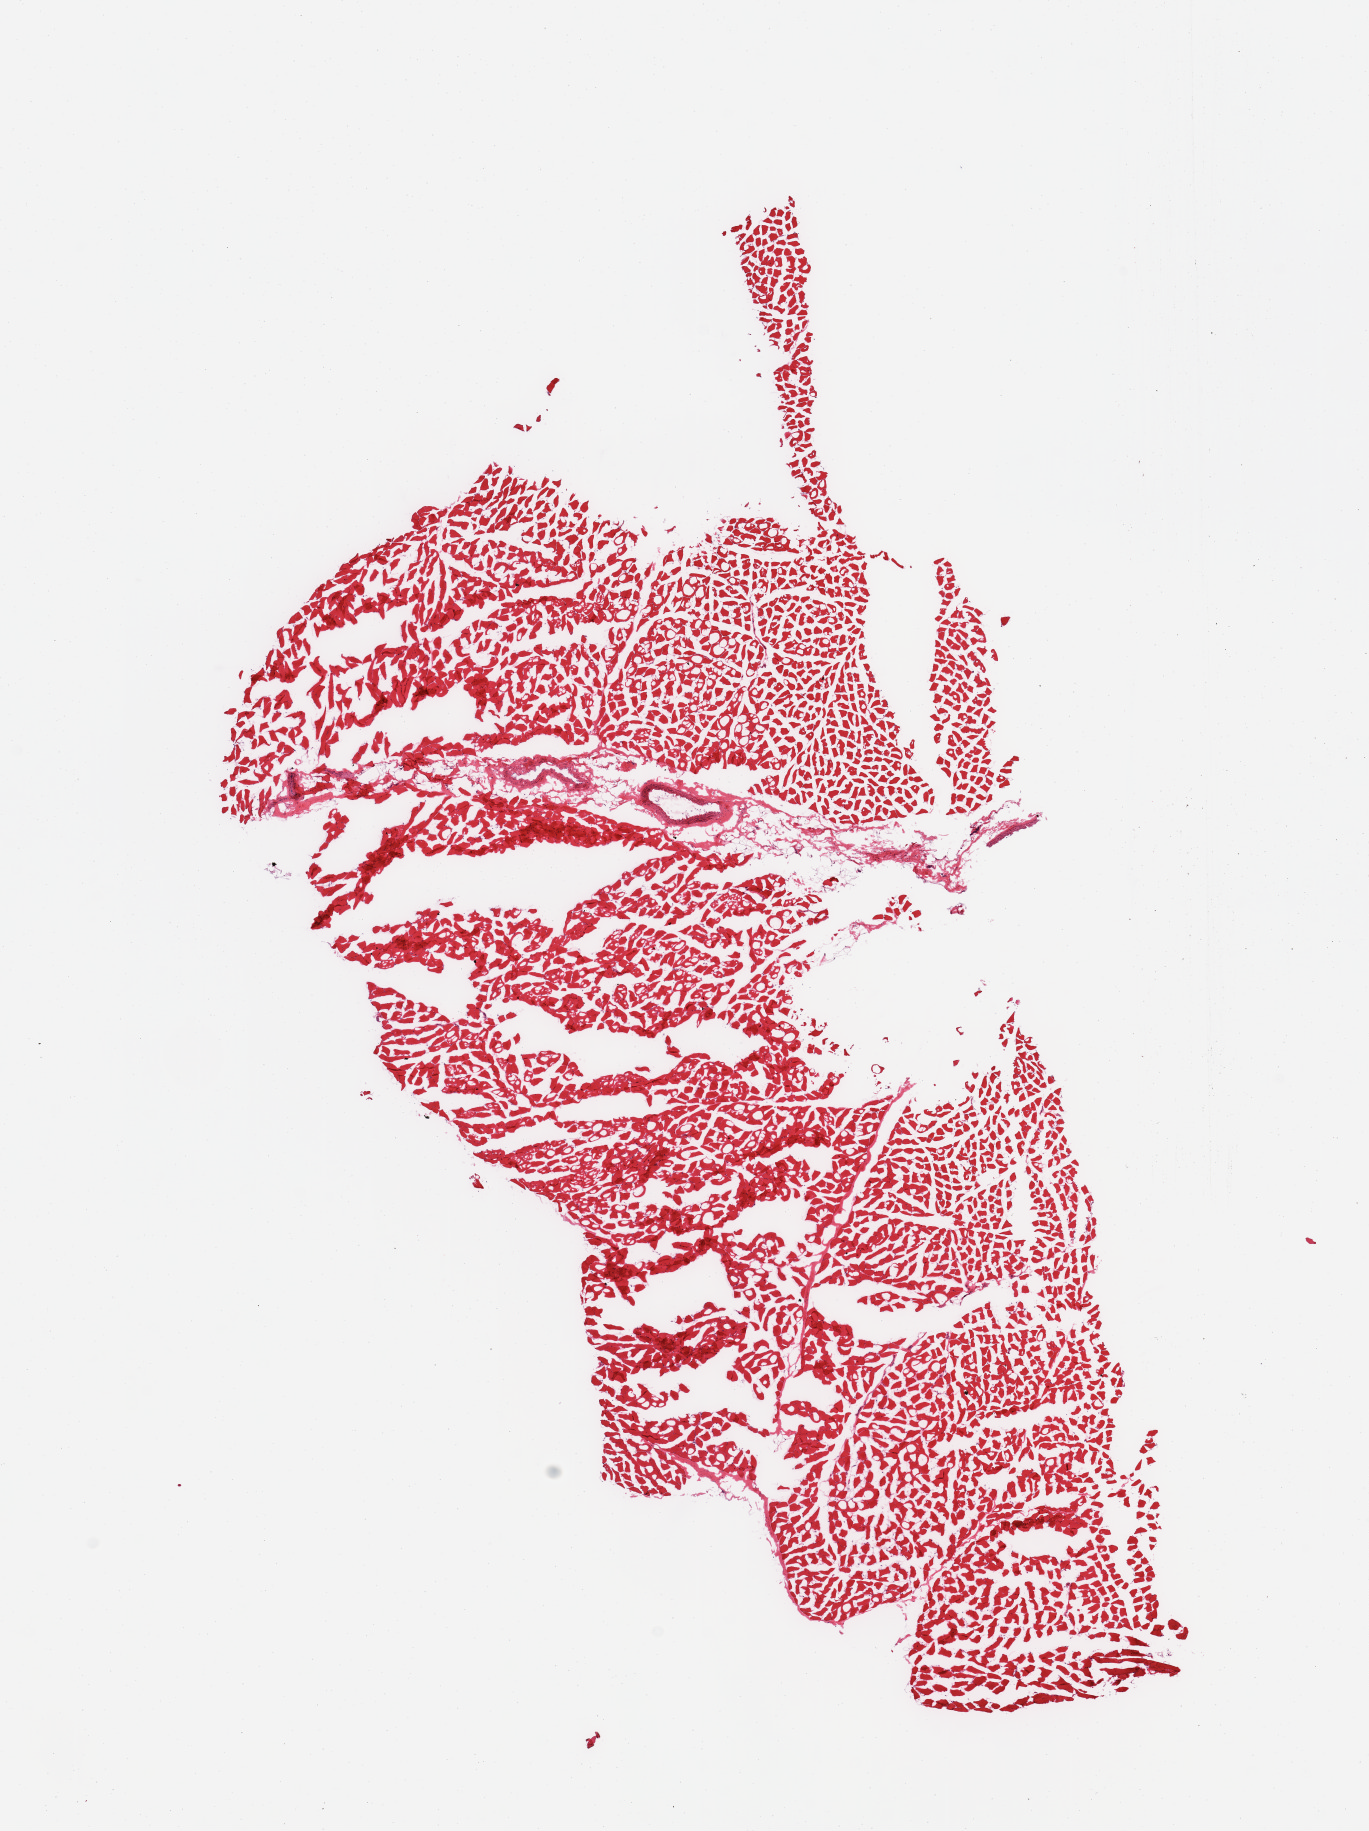
Digitized haematoxylin and eosin-stained section, brightfield — shown as a low-resolution overview of the whole scanned area (about 10.8 x 14.5 mm), frozen section, section of skeletal muscle (target tissue), tissue donor sample. Donor sex: male.
* pathologist's review note for this sample: 1 piece; comparable to PAXgene sample with 2 prominent blood vessels